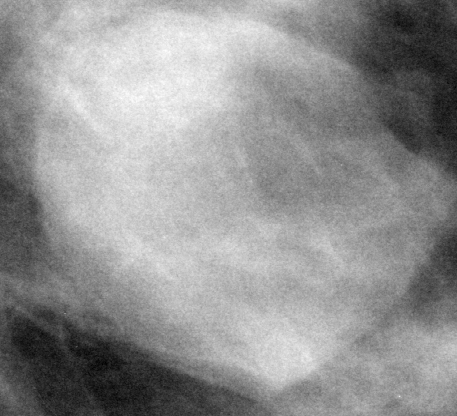
Crop from a digitized film mammogram around one marked abnormality; left breast; MLO view; BI-RADS breast density category 2 (scale 1–4).
Mass, shape oval, margins circumscribed; BI-RADS assessment category 3; pathology result (as recorded, not read from the image): benign.